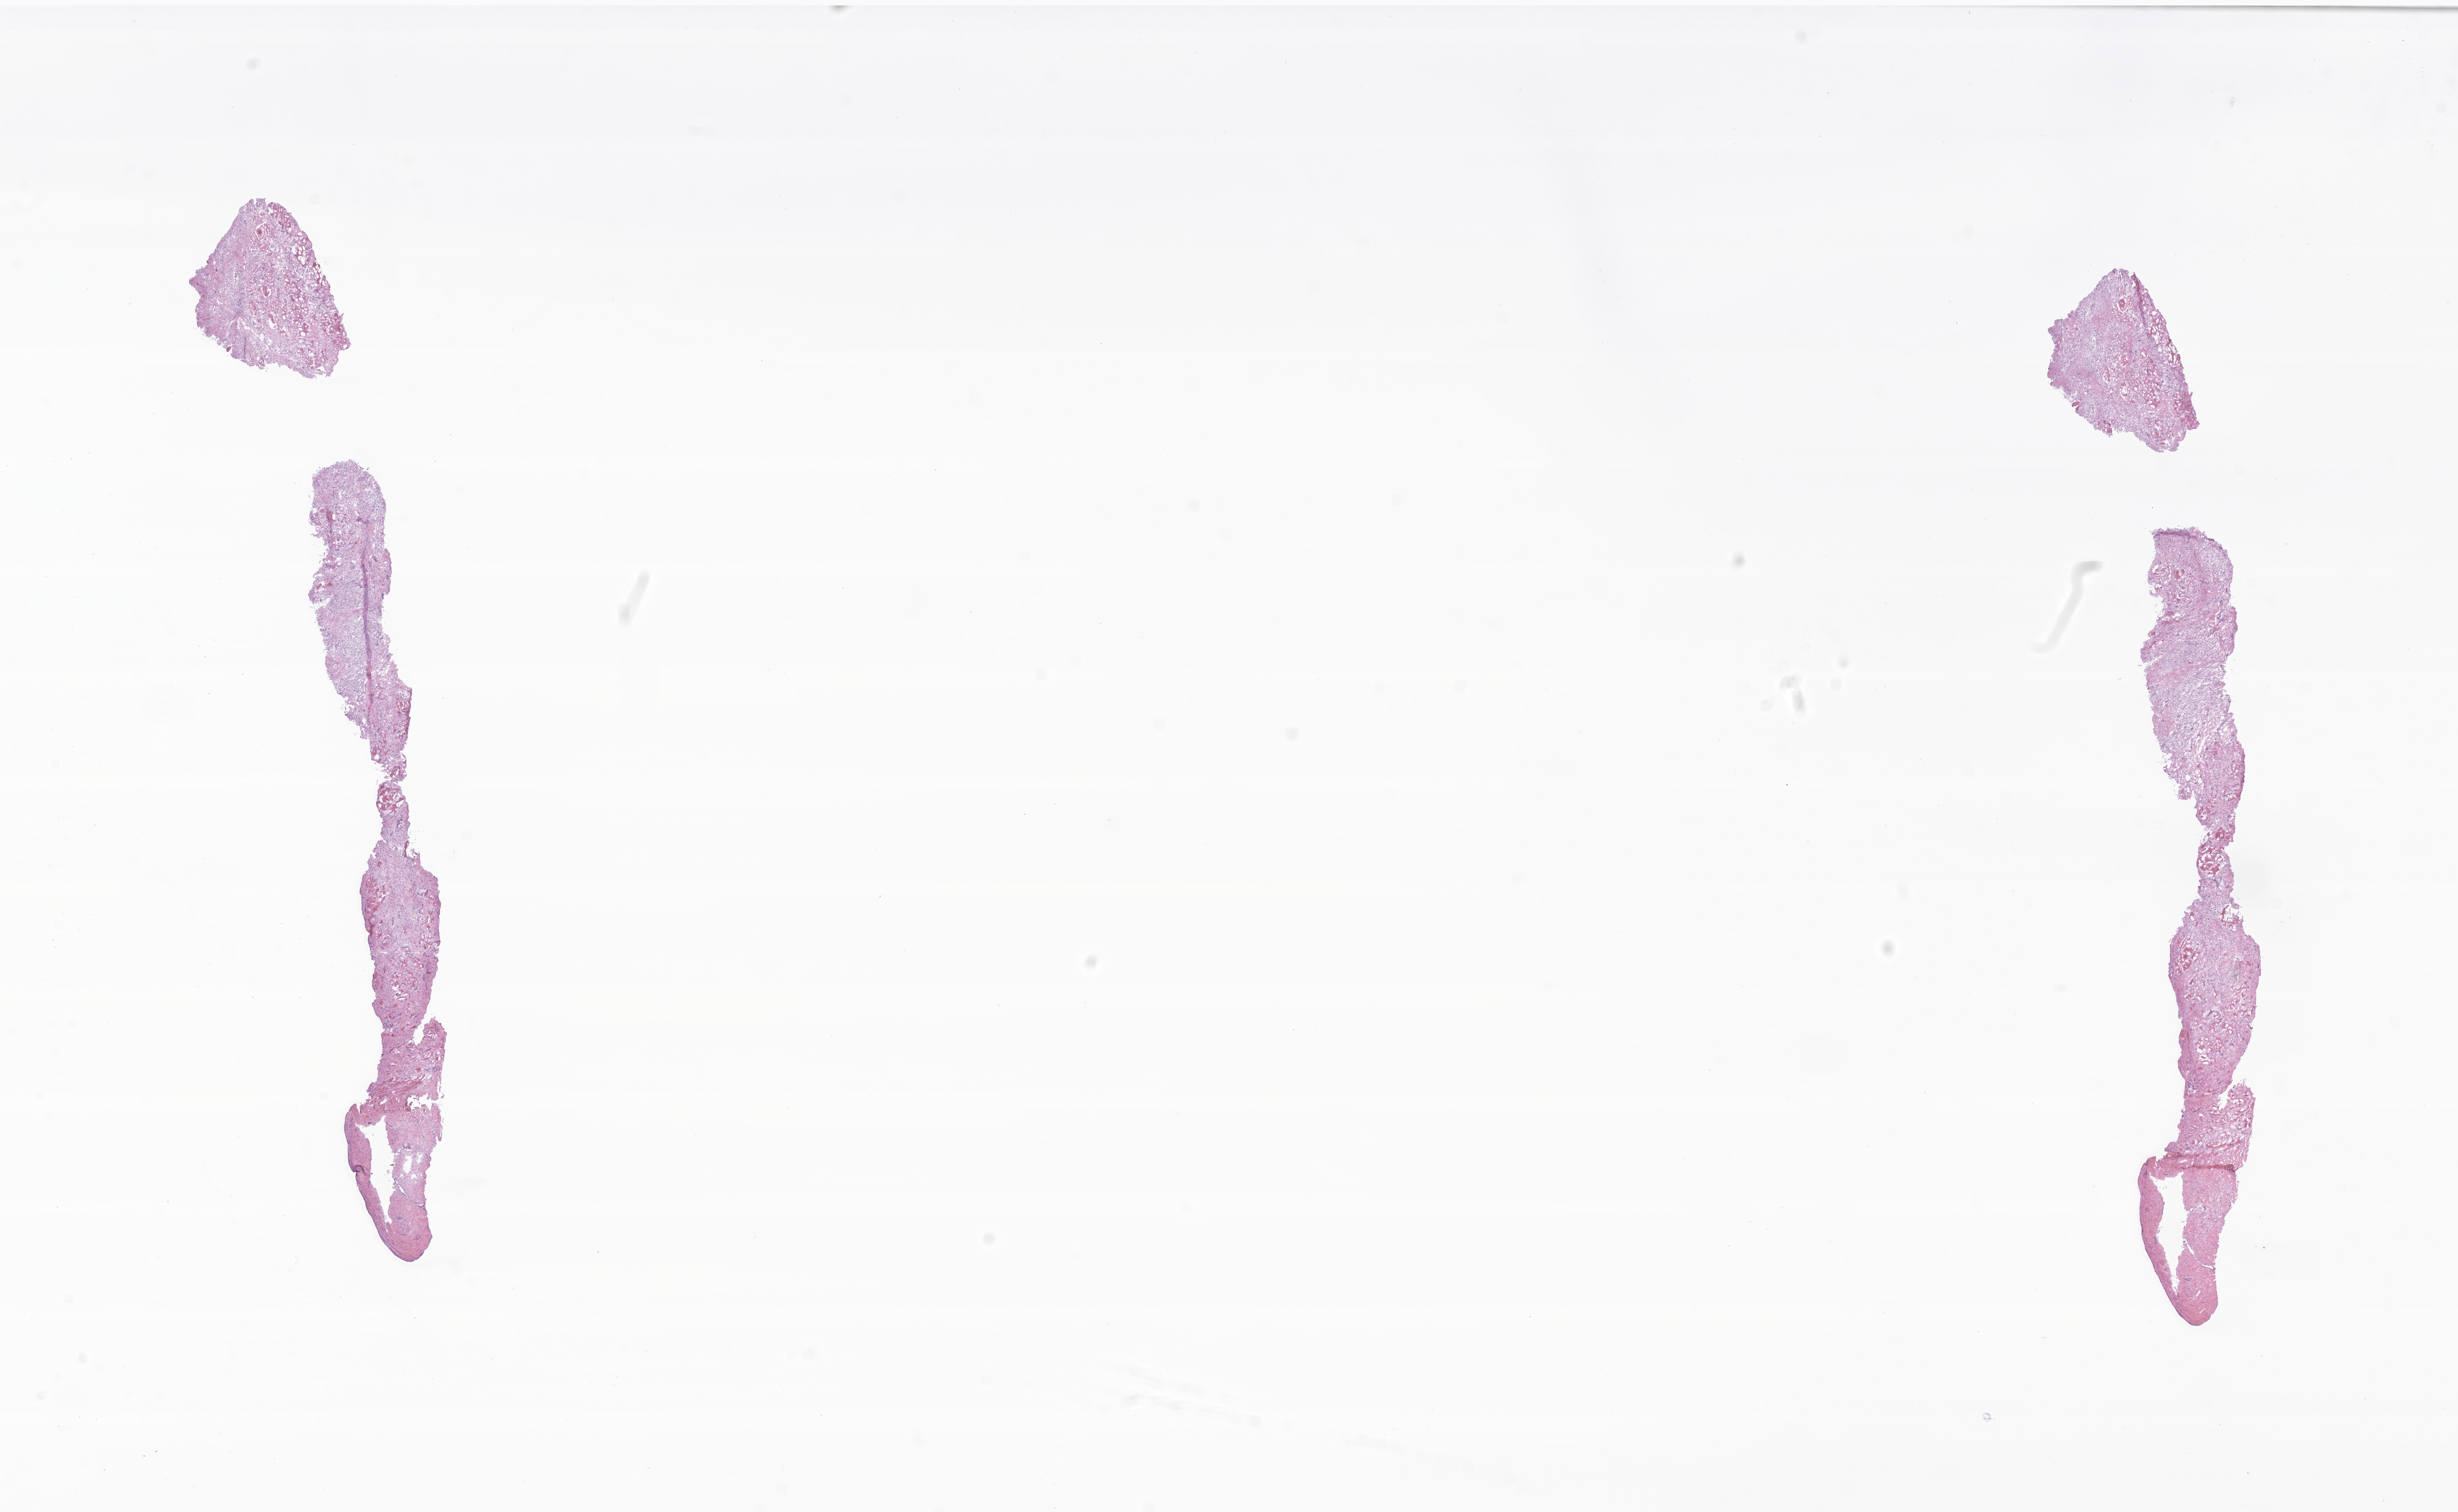
Whole-slide image, haematoxylin and eosin stain of tumor tissue from the soft tissue — shown as a low-resolution overview of the whole scanned area (about 24.7 x 15.2 mm); frozen section. Male patient, age 157 months (13 years 1 month).
- recorded diagnosis: Aggressive fibromatosis